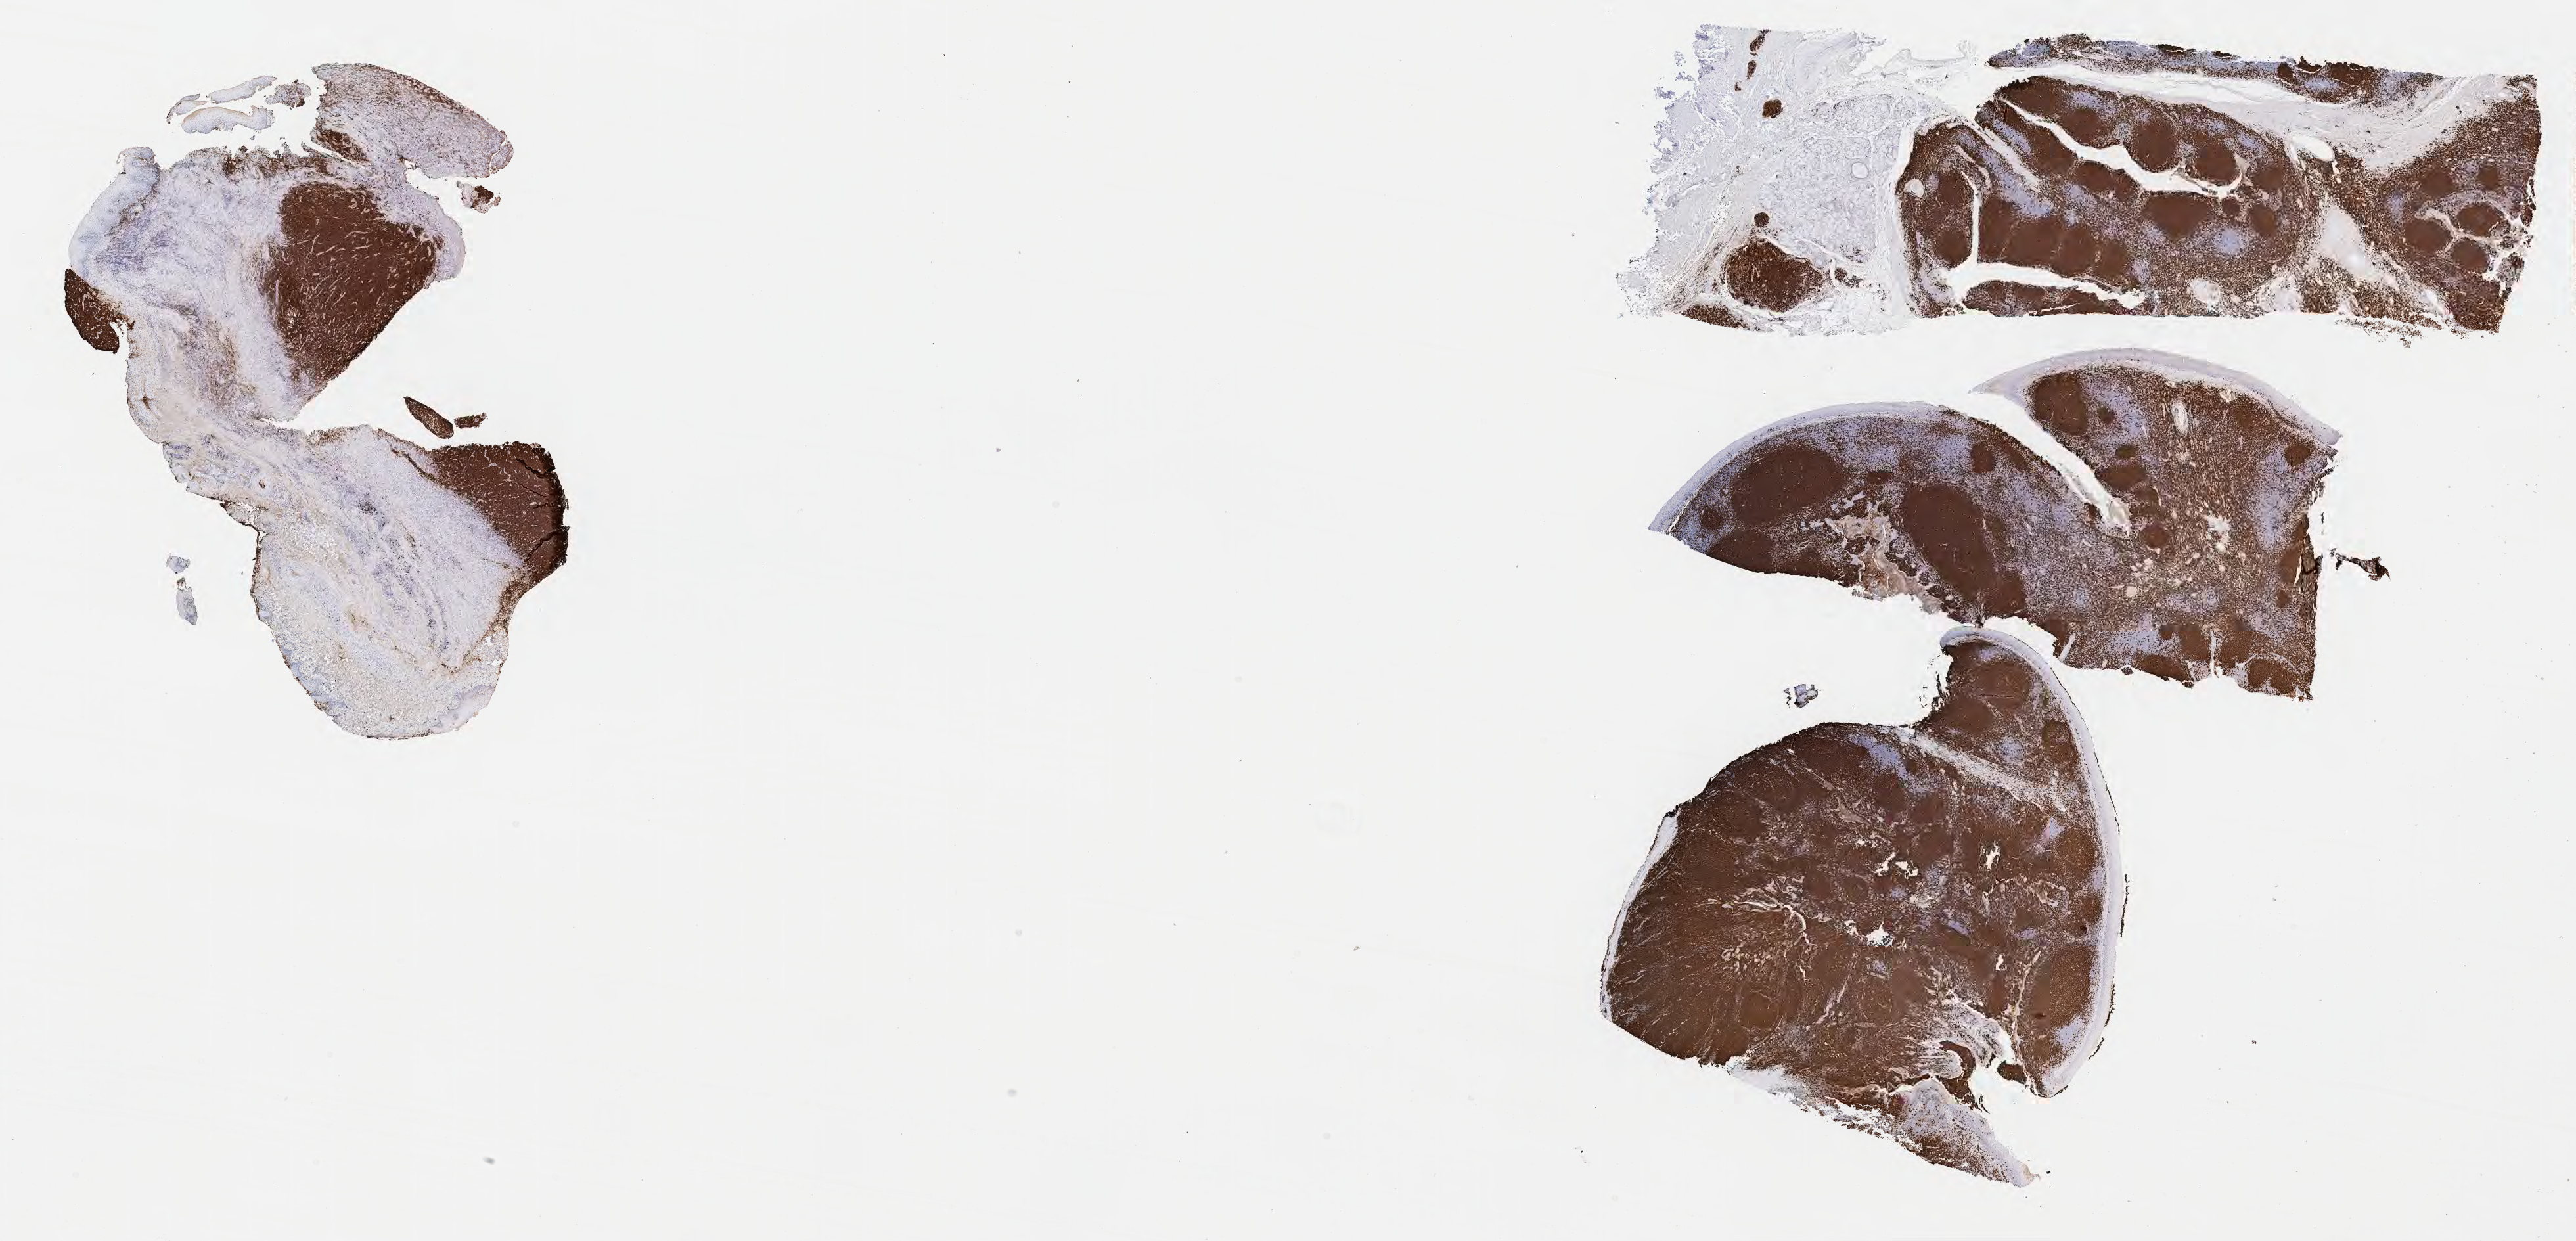
IHC for CD20, whole-slide image, shown as a low-resolution overview of the whole scanned area (about 31.7 x 15.3 mm). Specimen: tumor tissue. Anatomic site: cranium. Patient male; 10 years old.
Histologic diagnosis: Burkitt lymphoma, NOS.